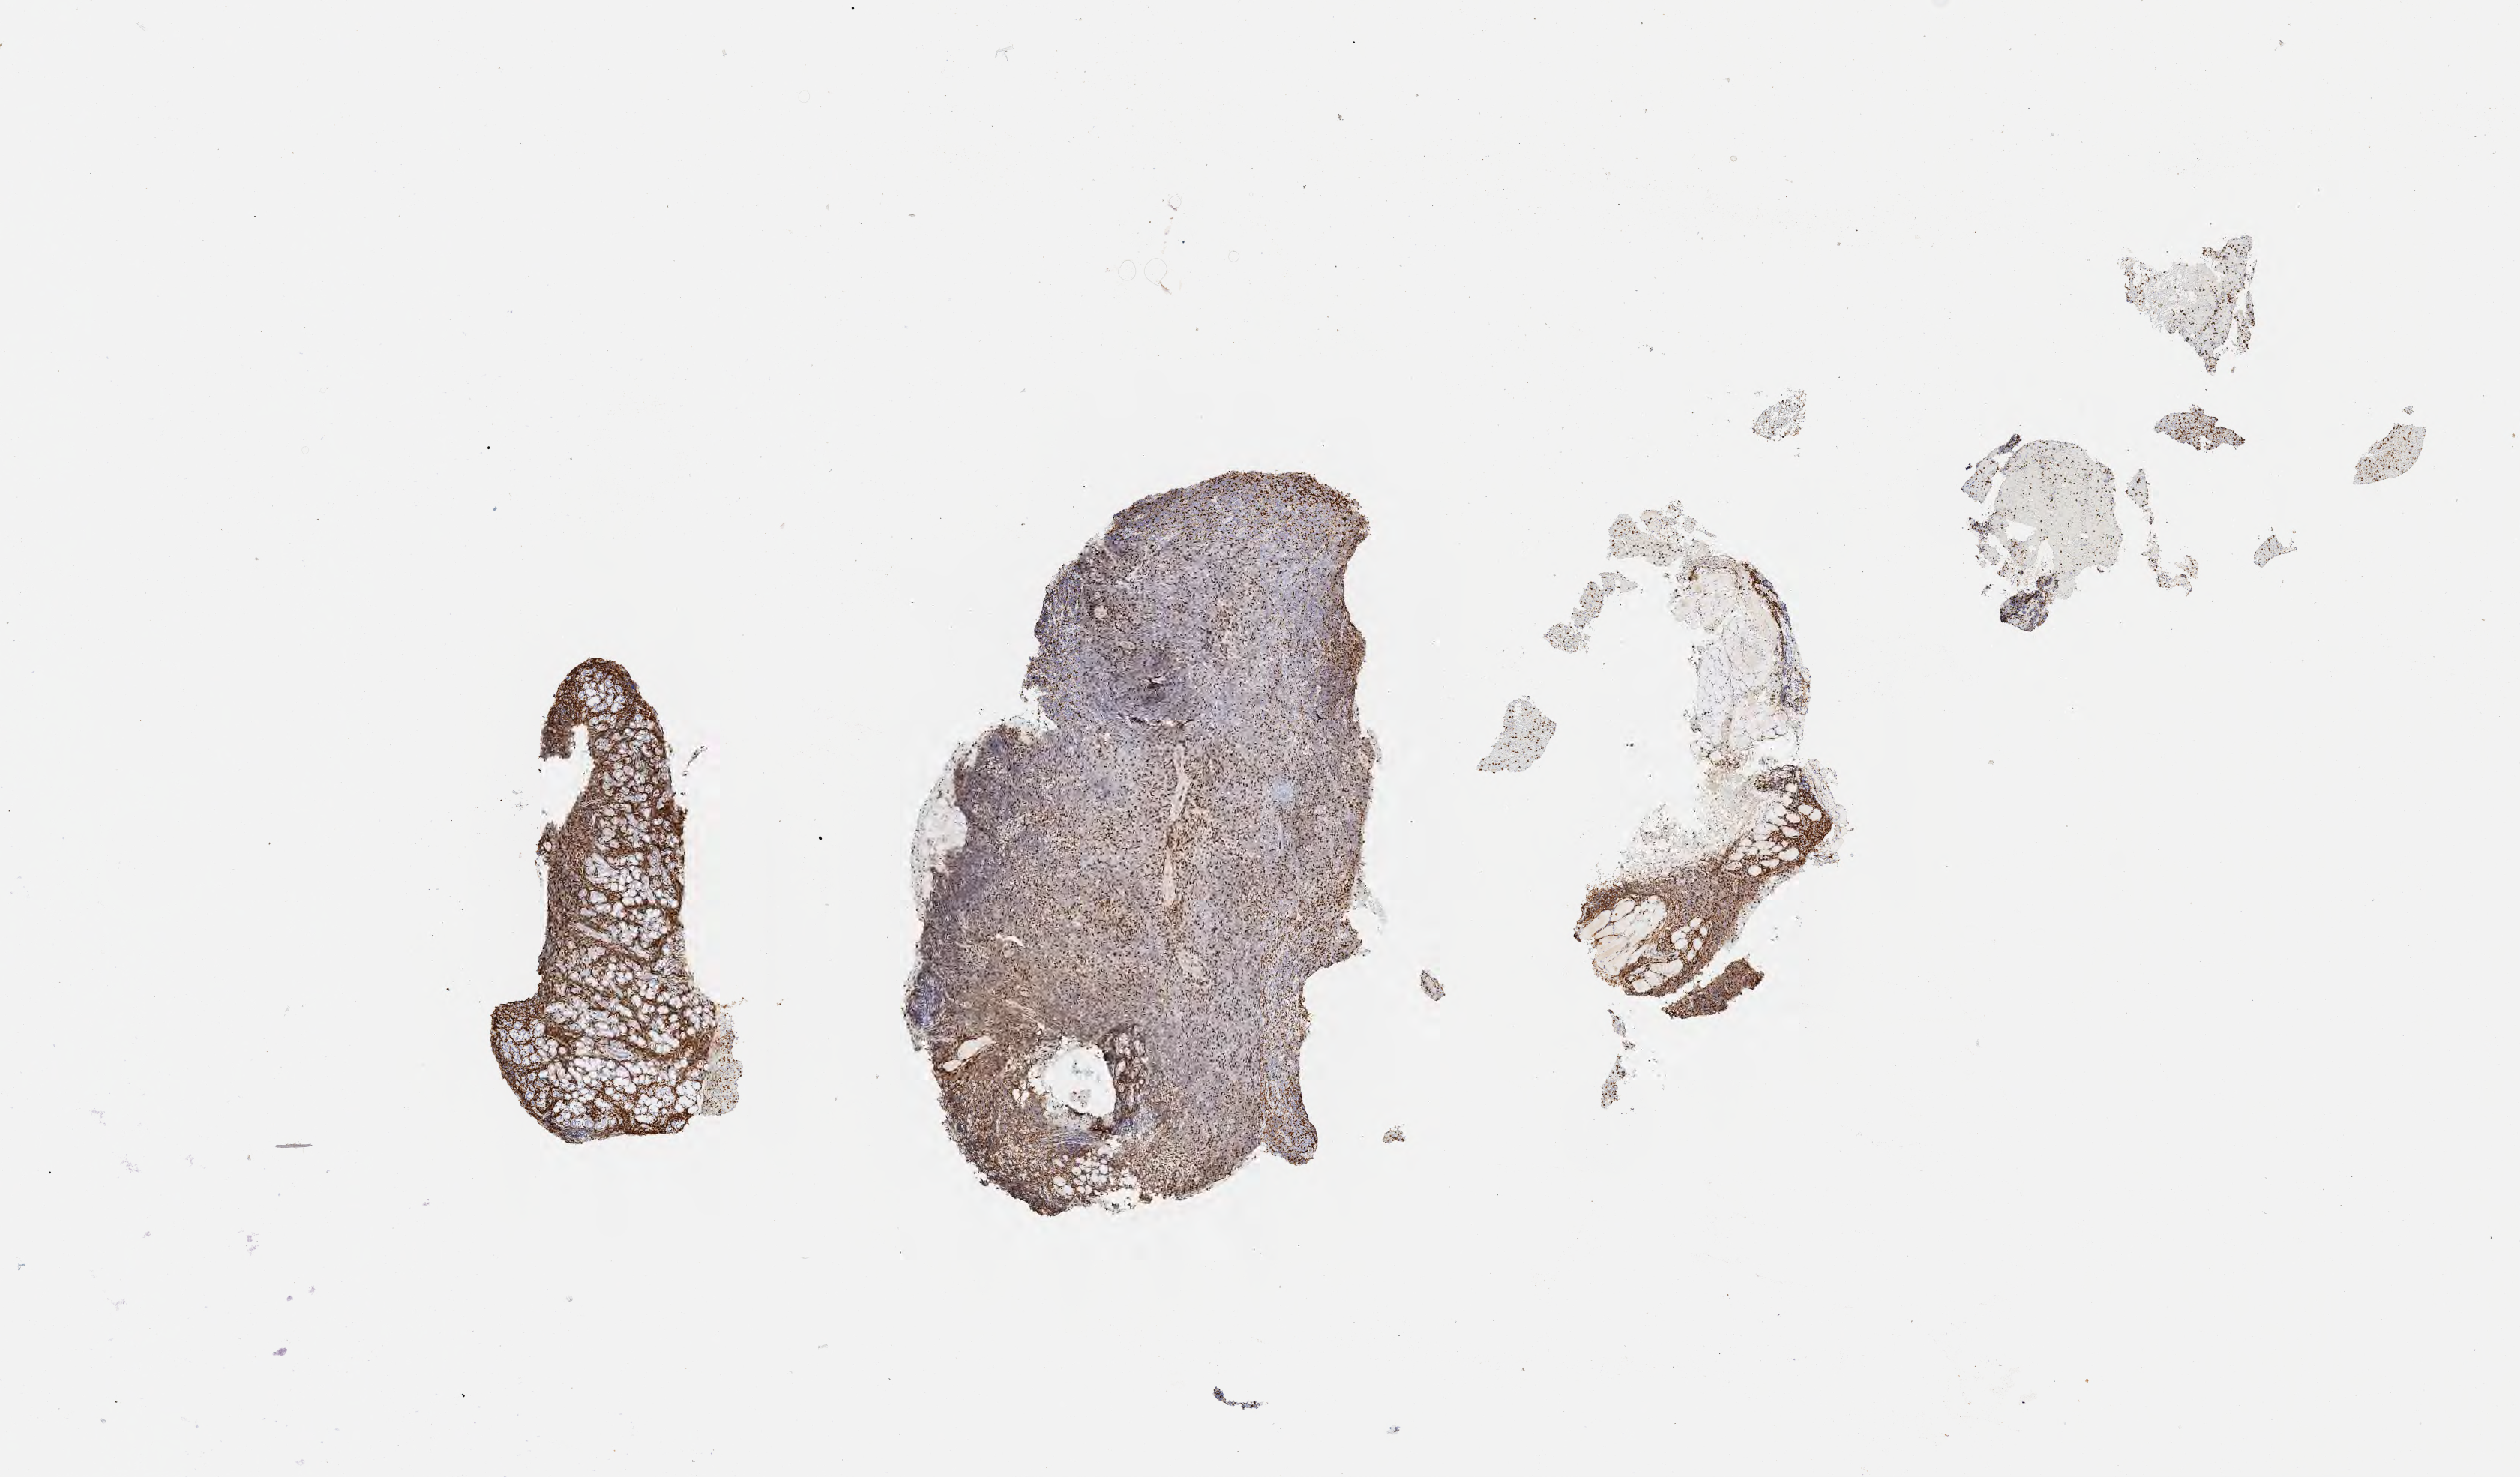
IHC for CD3, whole-slide image, low-resolution overview of the scanned area, about 13.6 x 8.0 mm. Tumor tissue. Male patient, 53 years old.
Histologic diagnosis: Diffuse large B-cell lymphoma, NOS.